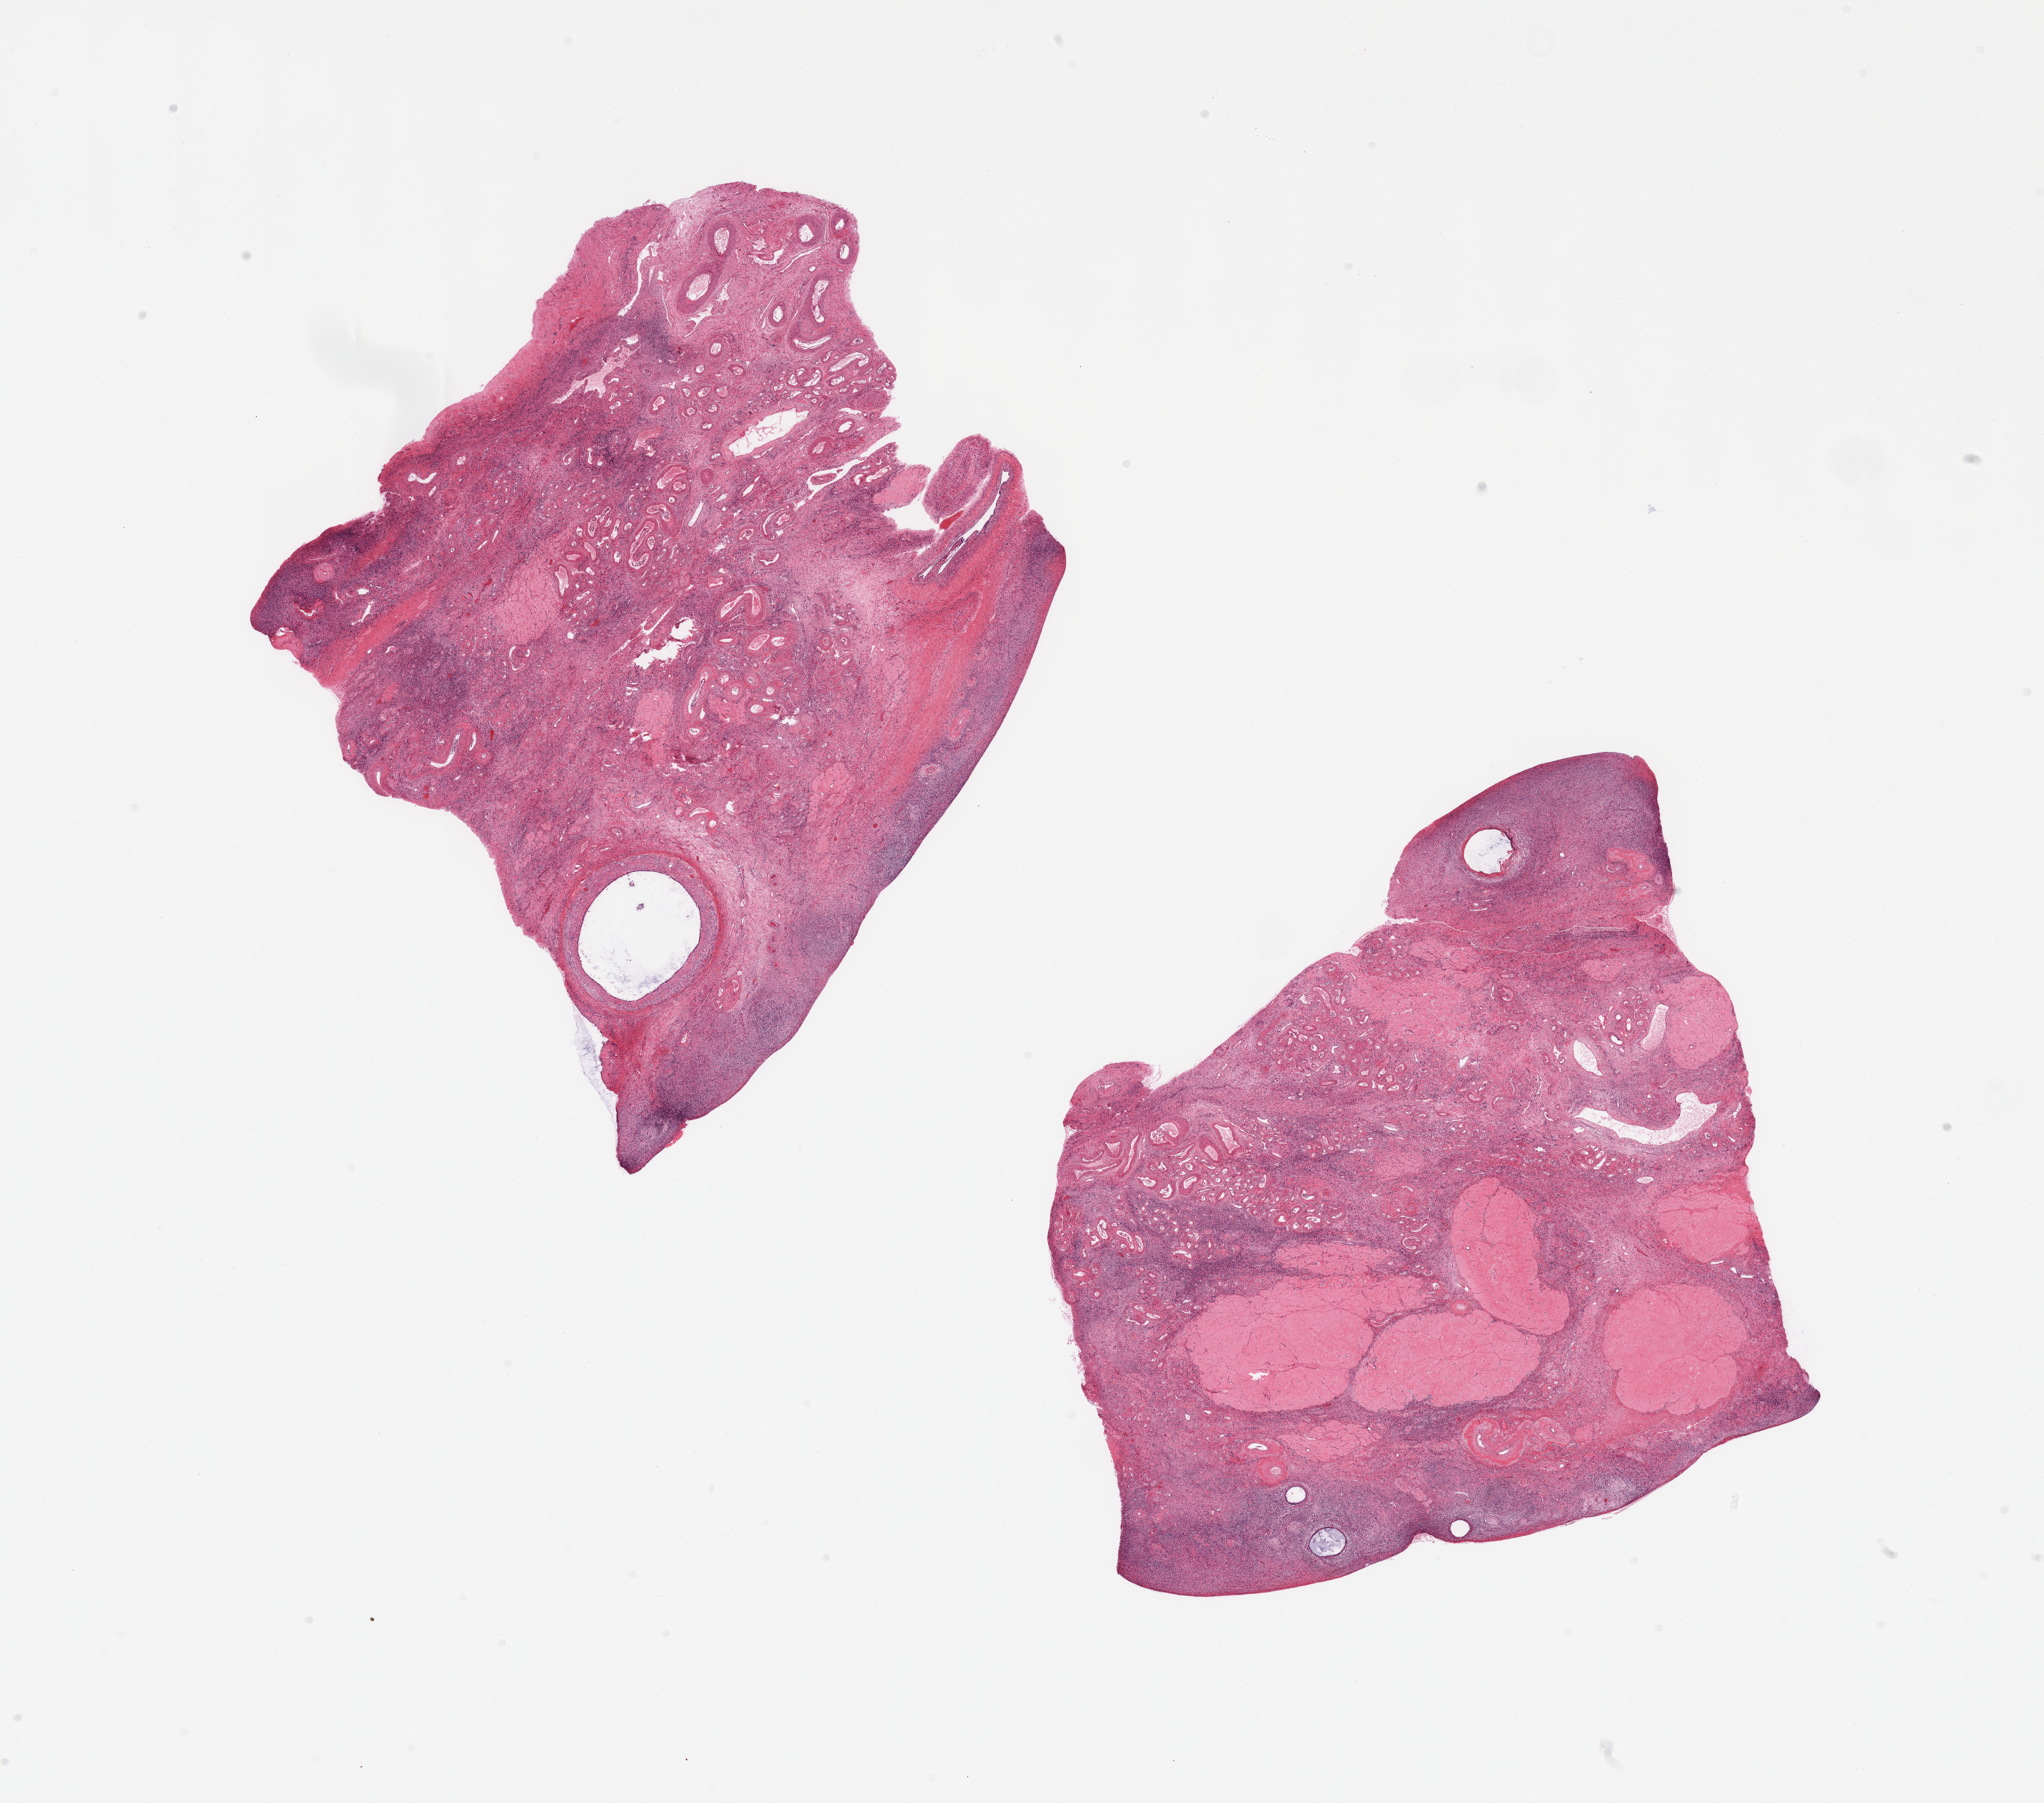
Haematoxylin and eosin whole-slide image, a low-resolution overview of the entire scanned area, about 22.6 x 20.0 mm; PAXgene-fixed, paraffin-embedded tissue; section of ovary (target tissue); donor tissue sample. Female donor.
• pathologist's review note for this sample: 2 pieces; atrophic with follicles and corpora albicans